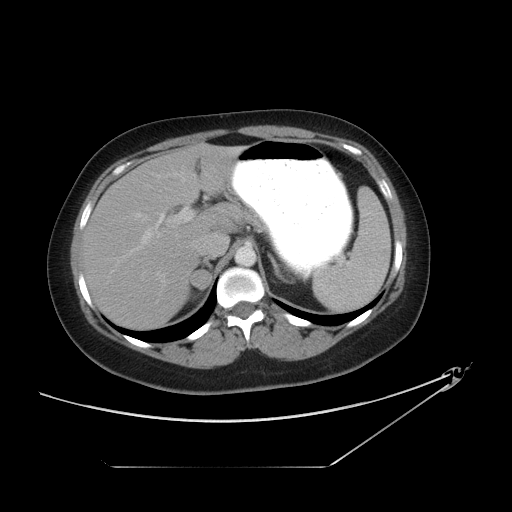
Contrast-enhanced abdominal CT, one axial slice; position 73 of 90 along the scan axis; reconstruction kernel STANDARD; intravenous contrast given; soft-tissue window (W 400 / L 40 HU); 5 mm slice thickness; 512 × 512 image matrix, field of view 437 × 437 mm. Female patient, age 45 years. Case-level facts recorded for this patient, not image findings: diagnosis: adrenocortical carcinoma; tumour side: right adrenal; tumour size at pathology: 2.5 cm; Ki-67 index: 25 %; stage (as recorded): 1.
Outlined on this slice (semi-automatic segmentation, software-assisted and operator-edited):
- mass: bounding box (x1, y1, x2, y2) in pixels: (190, 269, 211, 290)